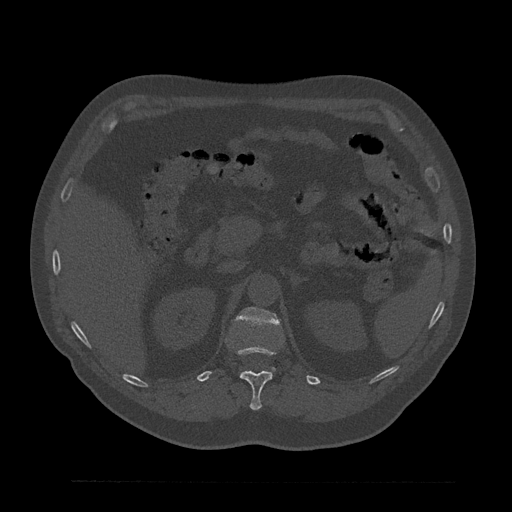
CT including the spine, one axial slice; position 208 of 797 along the scan axis; reconstruction kernel Br40s/3; bone window (W 1800 / L 400 HU); 512 × 512 image matrix. Male patient, age 61 years. Case-level facts recorded for this patient, not image findings: primary cancer: prostate.
Annotated regions visible in this slice (semi-automatic segmentation, software-assisted and operator-edited):
- L1 vertebra: bounding box (x1, y1, x2, y2) in pixels: (236, 307, 279, 325)
- T12 vertebra: (225, 339, 276, 410)